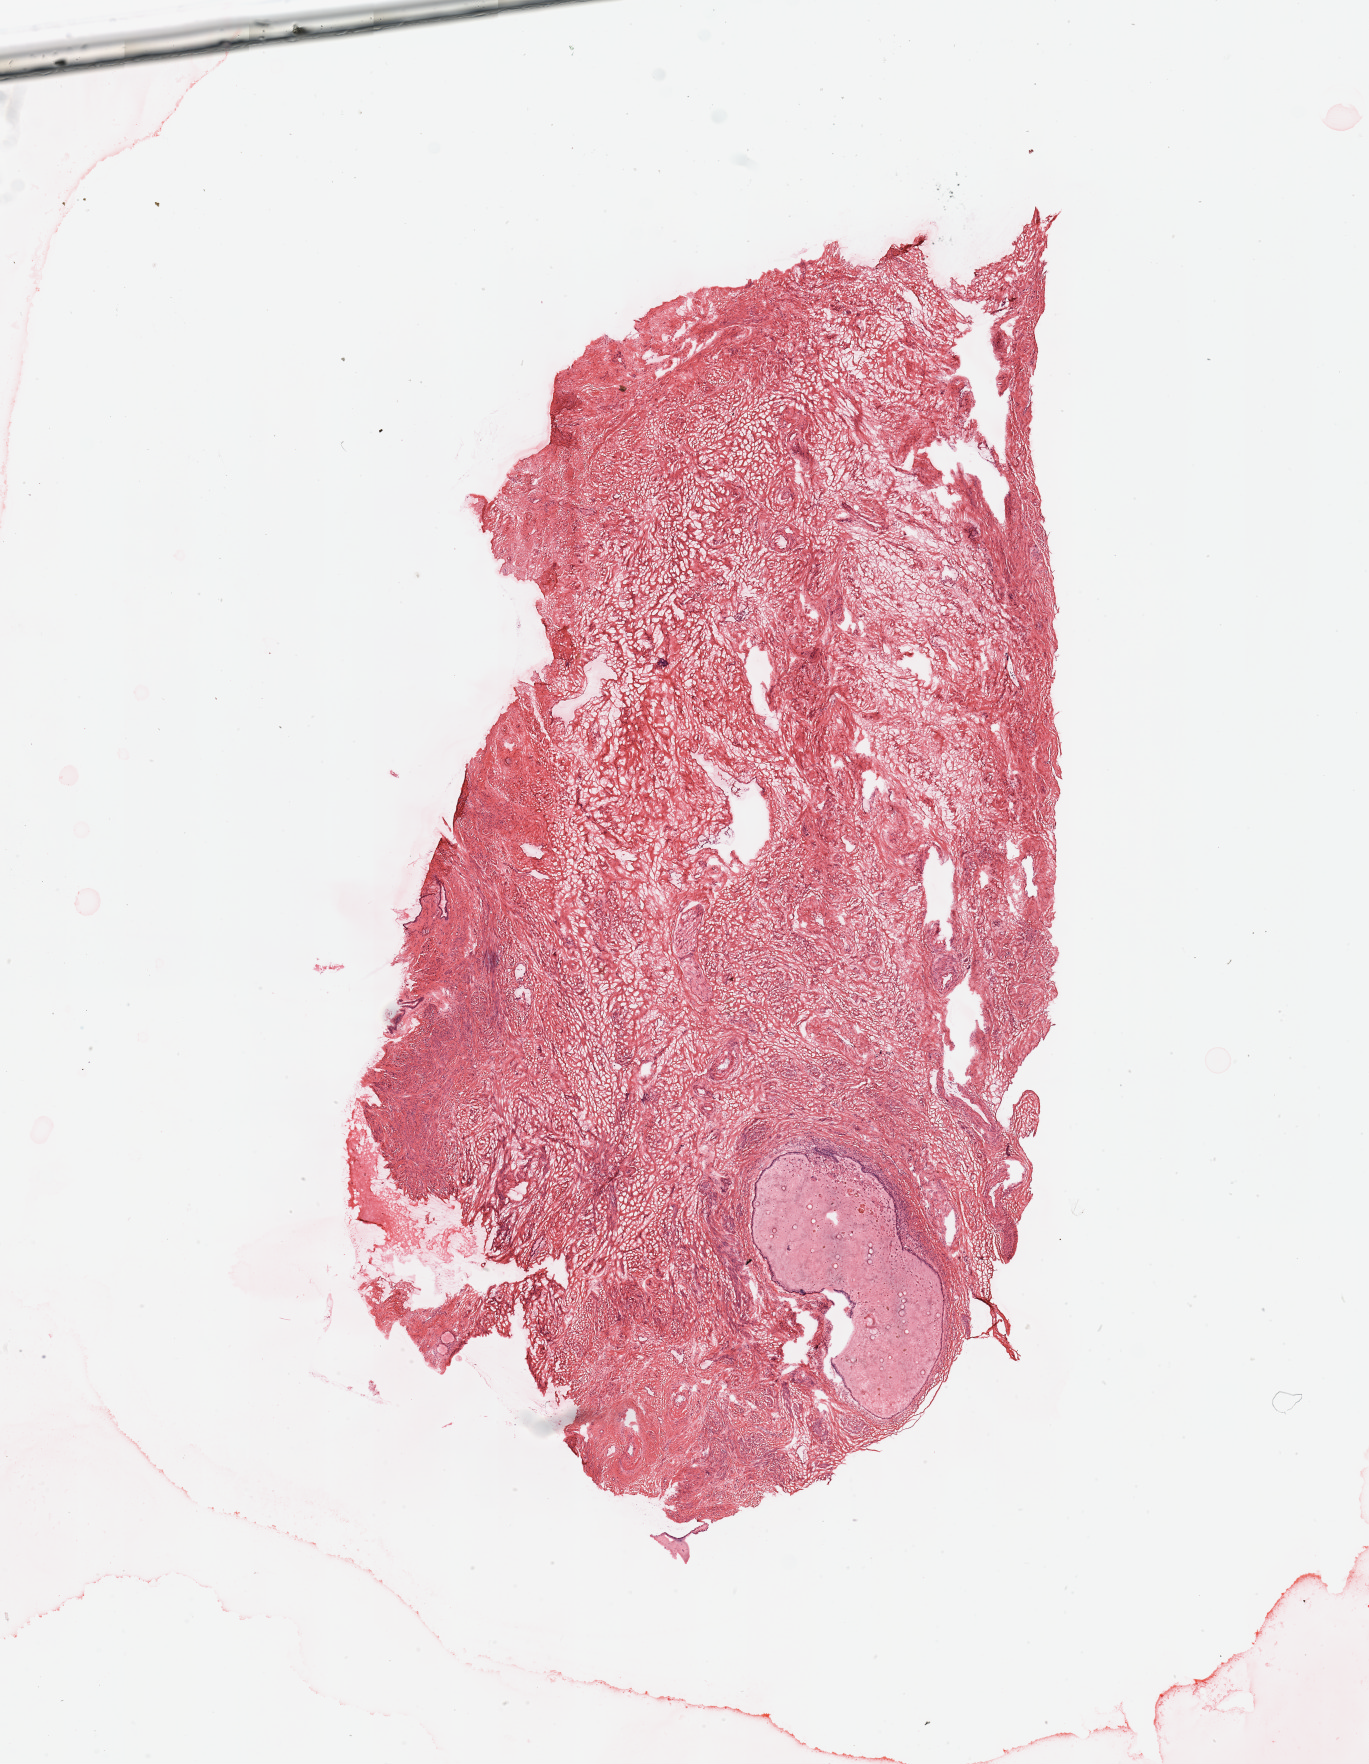
Whole-slide histology image, H&E-stained — a low-resolution overview of the entire scanned area, about 10.8 x 14.0 mm, normal (non-tumour) tissue sample, uterus. Female, 65 y/o.
This section: normal (non-tumour) tissue from the same patient. Patient diagnosis: Endometrioid adenocarcinoma, NOS.